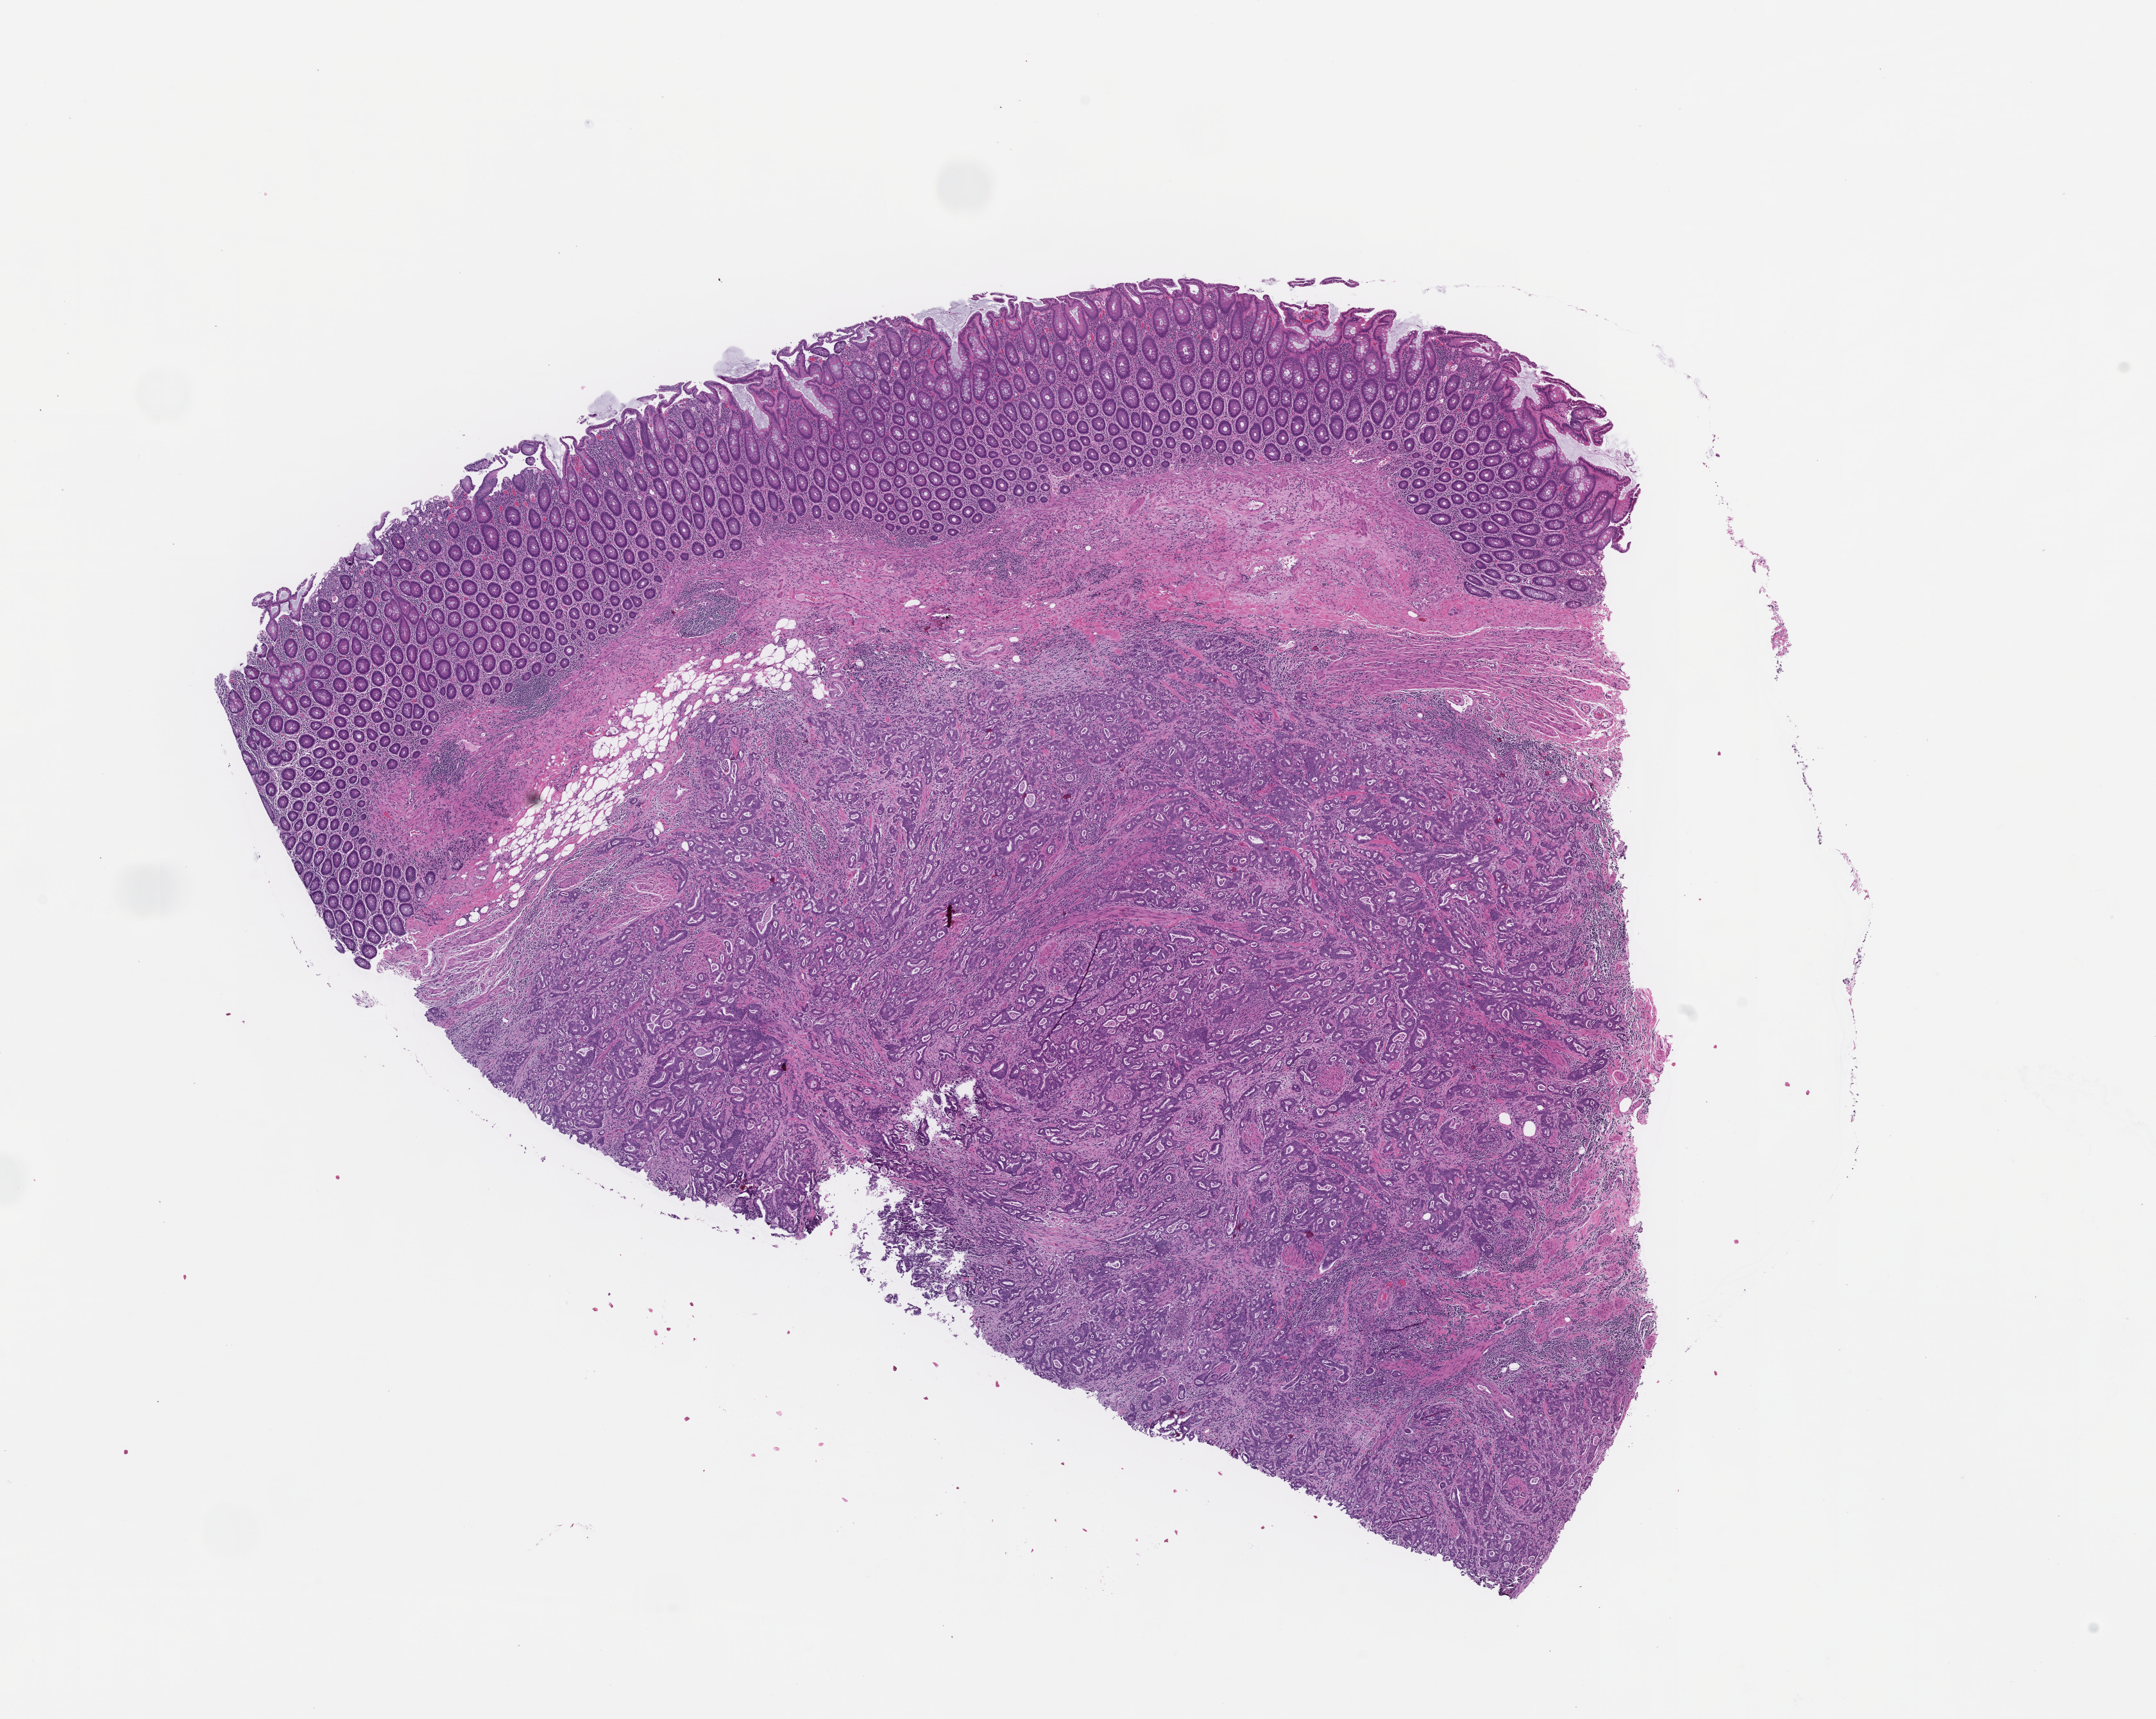
Whole-slide image, H&E stain, whole scanned area (about 13.6 x 10.8 mm) shown as a low-resolution overview. Formalin-fixed paraffin-embedded section. Specimen time point: collected at baseline (before treatment). Patient sex: female.
* this section: metastatic tumor tissue
* primary diagnosis of the patient: Colorectal Carcinoma